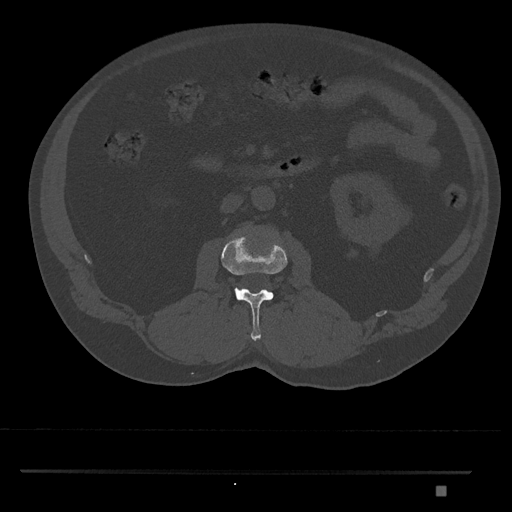
CT including the spine, one axial slice; position 738 of 1134 along the scan axis; reconstruction kernel Br40s/3; 120 kVp; bone window (W 1800 / L 400 HU); 0.5 mm slice thickness; 512 × 512 image matrix, field of view 429 × 429 mm. Male patient, age 65 years. Case-level facts recorded for this patient, not image findings: primary cancer: prostate.
Annotated regions visible in this slice (semi-automatic segmentation, software-assisted and operator-edited):
- L2 vertebra: bounding box [x1, y1, x2, y2] px = [221, 235, 288, 341]